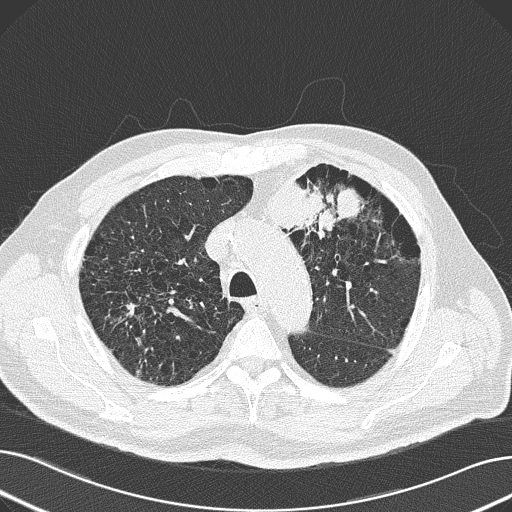
Chest CT (low-dose screening protocol), one axial image. First (baseline) screen. Lung window (W 1500 / L -600 HU). Lung (sharp) reconstruction kernel (B50f). 120 kVp. Slice 53 of 165 in the series. Male participant, aged 69 years at enrolment. Former smoker at enrolment.
Lesion marked by an expert reader, box from (x=225, y=150) to (x=379, y=255) px. Screening reader's record for this exam (one nodule recorded; not confirmed to be the boxed lesion): non-calcified nodule or mass ≥4 mm, left upper lobe, 6 × 10 mm, spiculated (stellate) margins, soft tissue attenuation. Lung cancer was diagnosed 20 days after this screen: non-small cell carcinoma, left upper lobe, poorly differentiated (G3), stage IB (AJCC 6th edition), 100 mm at pathology.